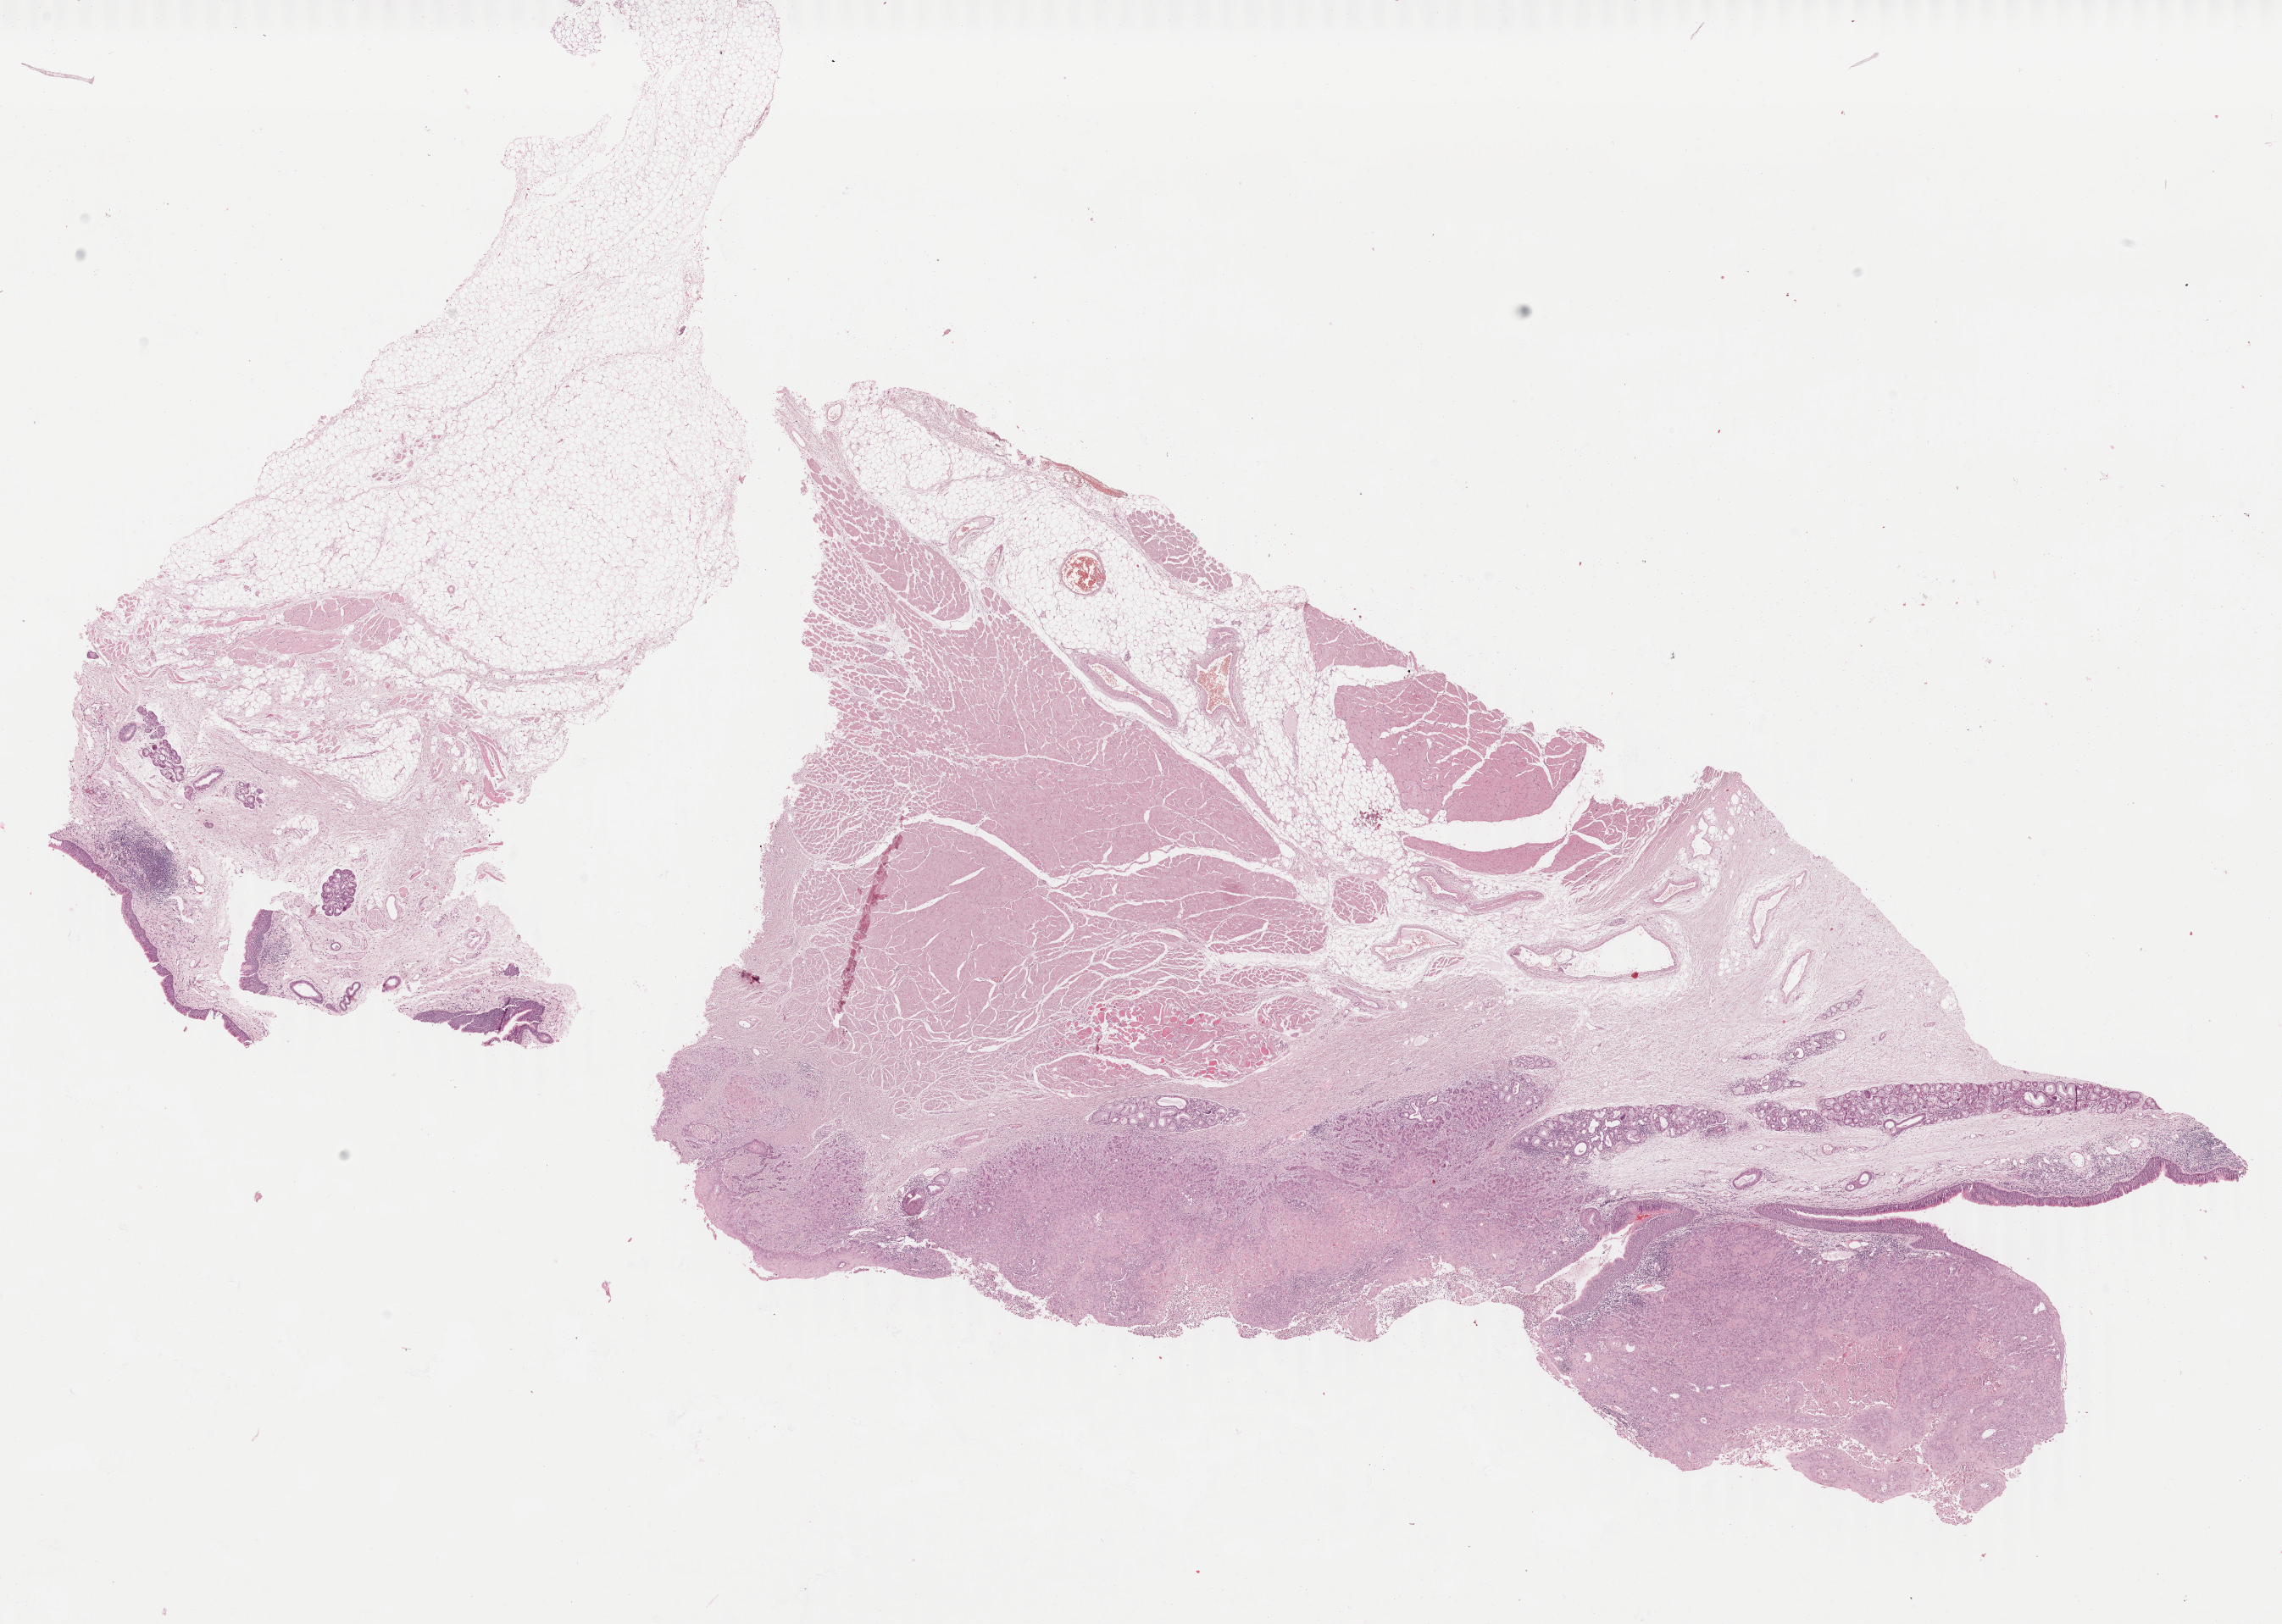
Digitized H&E-stained tissue section (whole slide), low-resolution overview of the scanned area, about 21.4 x 15.2 mm (acquisition: 40x scan); formalin-fixed paraffin-embedded (FFPE) diagnostic section; head and neck, primary tumour sample. Patient: female, age at initial diagnosis 64 years. Histologic grade: G2 (moderately differentiated).
TNM: T4a N2b. AJCC pathologic stage: IVA (7th edition). Histologic diagnosis: Squamous cell carcinoma, NOS (larynx, NOS).